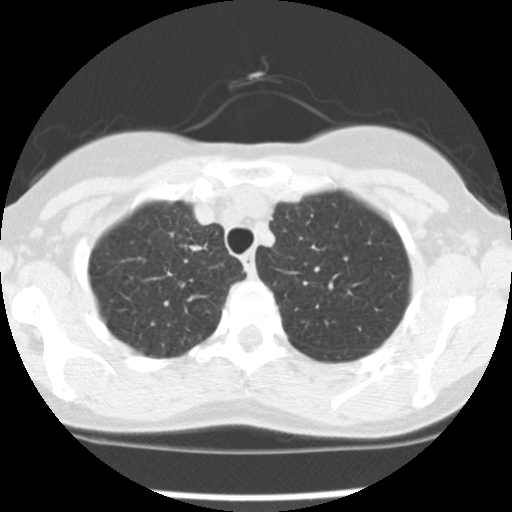
Low-dose screening chest CT, one axial slice. Reconstruction kernel STANDARD. 120 kVp. Lung window (W 1500 / L -600 HU). 2.5 mm slice thickness. 512 × 512 image matrix, field of view 282 × 282 mm.
Annotated regions visible in this slice (expert manual segmentation):
- lesion 1 (tumor, upper lobe of right lung): bounding box (x1, y1, x2, y2) in pixels: (189, 245, 204, 251)